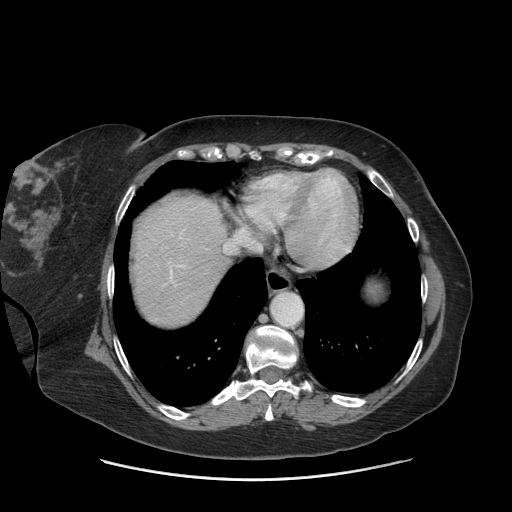
Contrast-enhanced abdominal CT (liver protocol), one axial slice. Position 65 of 69 along the scan axis. Reconstruction kernel STANDARD. Soft-tissue window (W 400 / L 40 HU). 2.5 mm slice thickness. 512 × 512 image matrix, field of view 420 × 420 mm. Case-level facts recorded for this patient, not image findings: diagnosis: hepatocellular carcinoma (patient treated with transarterial chemoembolisation; whether this scan precedes or follows treatment is not stated here); TNM stage (as recorded): Stage-IIIB.
Structures marked on this image (semi-automatic segmentation, software-assisted and operator-edited):
- abdominal aorta: bounding box (x1, y1, x2, y2) in pixels: (272, 294, 302, 326)
- liver parenchyma outside the tumour (the mass and vessels are separate outlines, so this box may not span the whole liver): (134, 196, 228, 324)
- liver vessels: (170, 265, 184, 278)